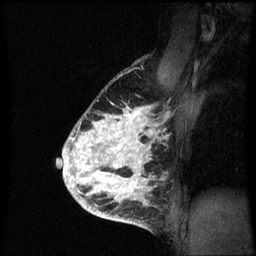
Breast MRI (dynamic contrast-enhanced), one sagittal slice; slice 46 of 60 in the series (ordered by position); dynamic contrast-enhanced series, image 2 of 3 at this slice position (ordered by acquisition); 1.5 T; TE 4.2 ms, TR 8.9 ms; 2 mm slice thickness; 256 × 256 image matrix, field of view 200 × 200 mm. Patient: female, 35 years. Case-level facts recorded for this patient, not image findings: setting: breast cancer imaged before/during neoadjuvant chemotherapy; receptor status: HR-positive, HER2-negative.
Annotated regions visible in this slice (semi-automatically segmented with operator editing):
- analysis volume of interest (the breast-tissue region the enhancement analysis was run in; not a lesion): bounding box (x1, y1, x2, y2) in pixels: (66, 102, 167, 215)
- tumour enhancement mask (voxels above the 70 % enhancement threshold inside the analysis volume of interest): (66, 108, 158, 215)